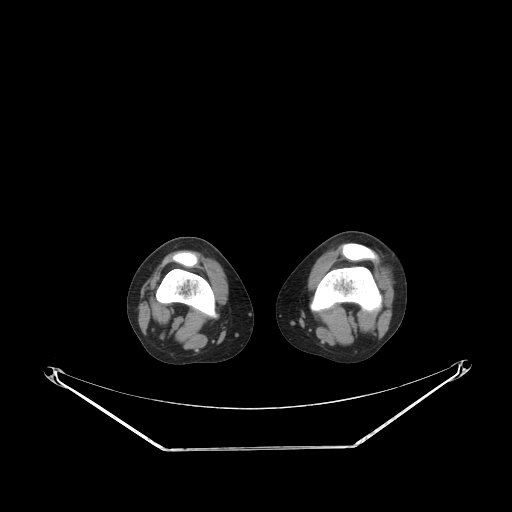
CT of an extremity soft-tissue mass (from a PET/CT study), one axial slice; position 167 of 223 along the scan axis; soft-tissue window (W 400 / L 40 HU); 512 × 512 image matrix, field of view 500 × 500 mm. Female patient. From the clinical record (not read from this slice): histological type: spindle cell suggestive of biphasic synovial sarcoma; grade: intermediate; site of the primary tumour: left knee.
Structures marked on this image (expert contour drawn on MRI and transferred to this co-registered scan by the dataset authors):
- gross tumour volume including surrounding oedema: bounding box <375,272,391,303> (left, top, right, bottom; pixels)
- gross tumour volume (mass): <375,274,391,303>